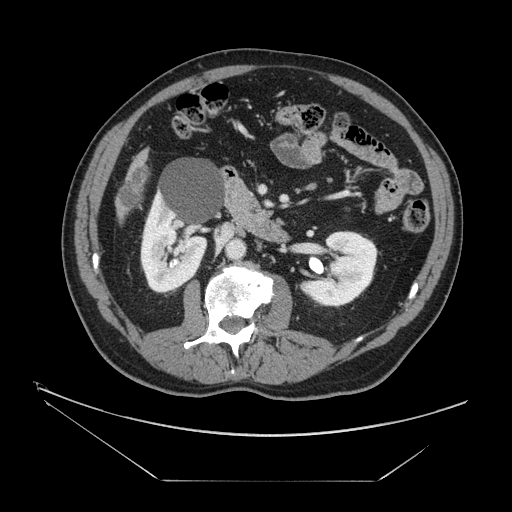
Contrast-enhanced abdominal CT, one axial slice; slice 50 of 161 in the series (ordered by position); reconstruction kernel STANDARD; intravenous contrast given; soft-tissue window (W 400 / L 40 HU); 2.5 mm slice thickness; 512 × 512 image matrix, field of view 440 × 440 mm. Male patient, age 65 years. Case-level facts recorded for this patient, not image findings: diagnosis: colorectal cancer liver metastases, imaged before liver resection; multiple liver metastases: yes; largest metastasis: 4.2 cm.
Structures marked on this image (outlined manually by an expert reader):
- liver: box from (x=120, y=155) to (x=146, y=214) px